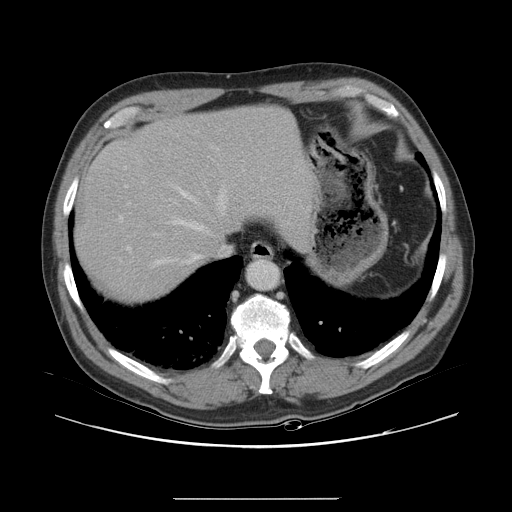
Contrast-enhanced abdominal CT, one axial slice; slice 26 of 40 in the series (ordered by position); intravenous contrast given; soft-tissue window (W 400 / L 40 HU); 5 mm slice thickness; 512 × 512 image matrix, field of view 408 × 408 mm. Male patient, age 64 years. Case-level facts recorded for this patient, not image findings: diagnosis: colorectal cancer liver metastases, imaged before liver resection.
Structures marked on this image (expert manual segmentation):
- hepatic veins: bounding box (x1, y1, x2, y2) in pixels: (128, 188, 225, 267)
- liver: (76, 109, 311, 301)
- planned liver remnant (the part of the liver to remain after resection): (77, 110, 311, 270)
- portal vein (with intrahepatic branches): (119, 148, 221, 249)